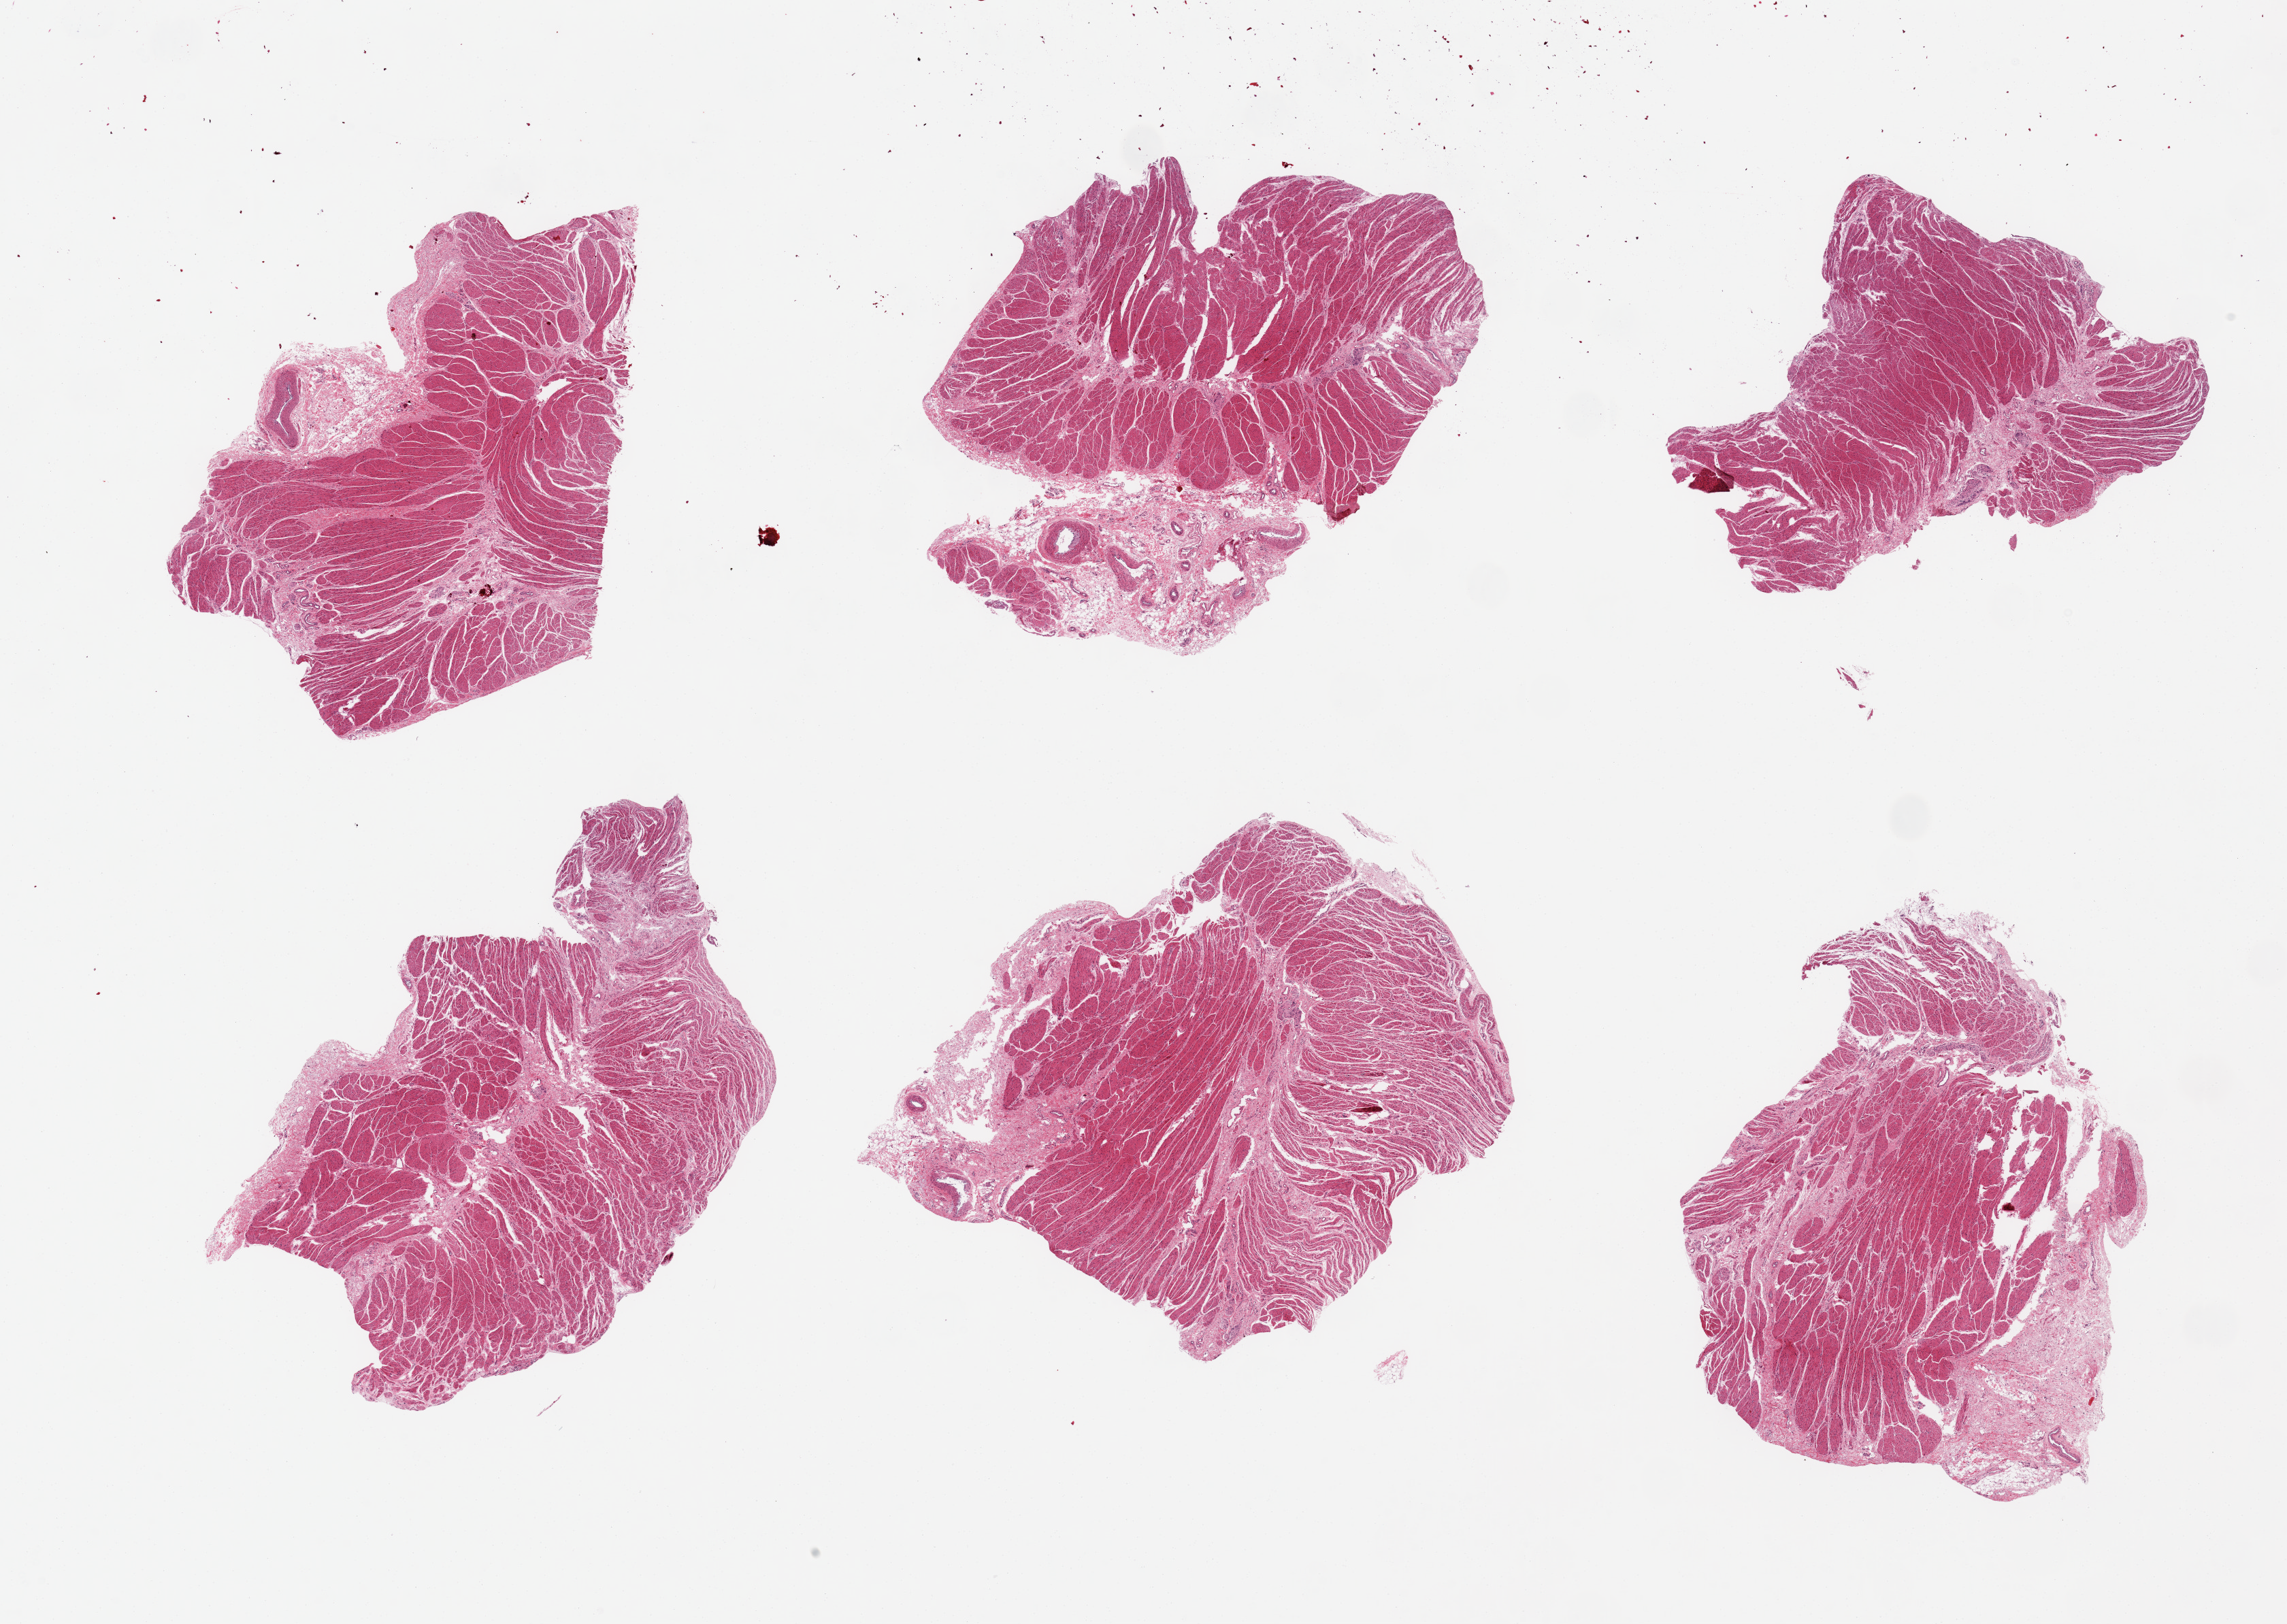
Whole-slide image, H&E stain, low-resolution overview of the scanned area, about 26.6 x 18.9 mm, PAXgene-fixed paraffin-embedded (PFPE) section, sampled site (target tissue): gastroesophageal junction, donor tissue sample. Donor sex: male.
- pathologist's review note for this sample: 6 pieces; target muscularis